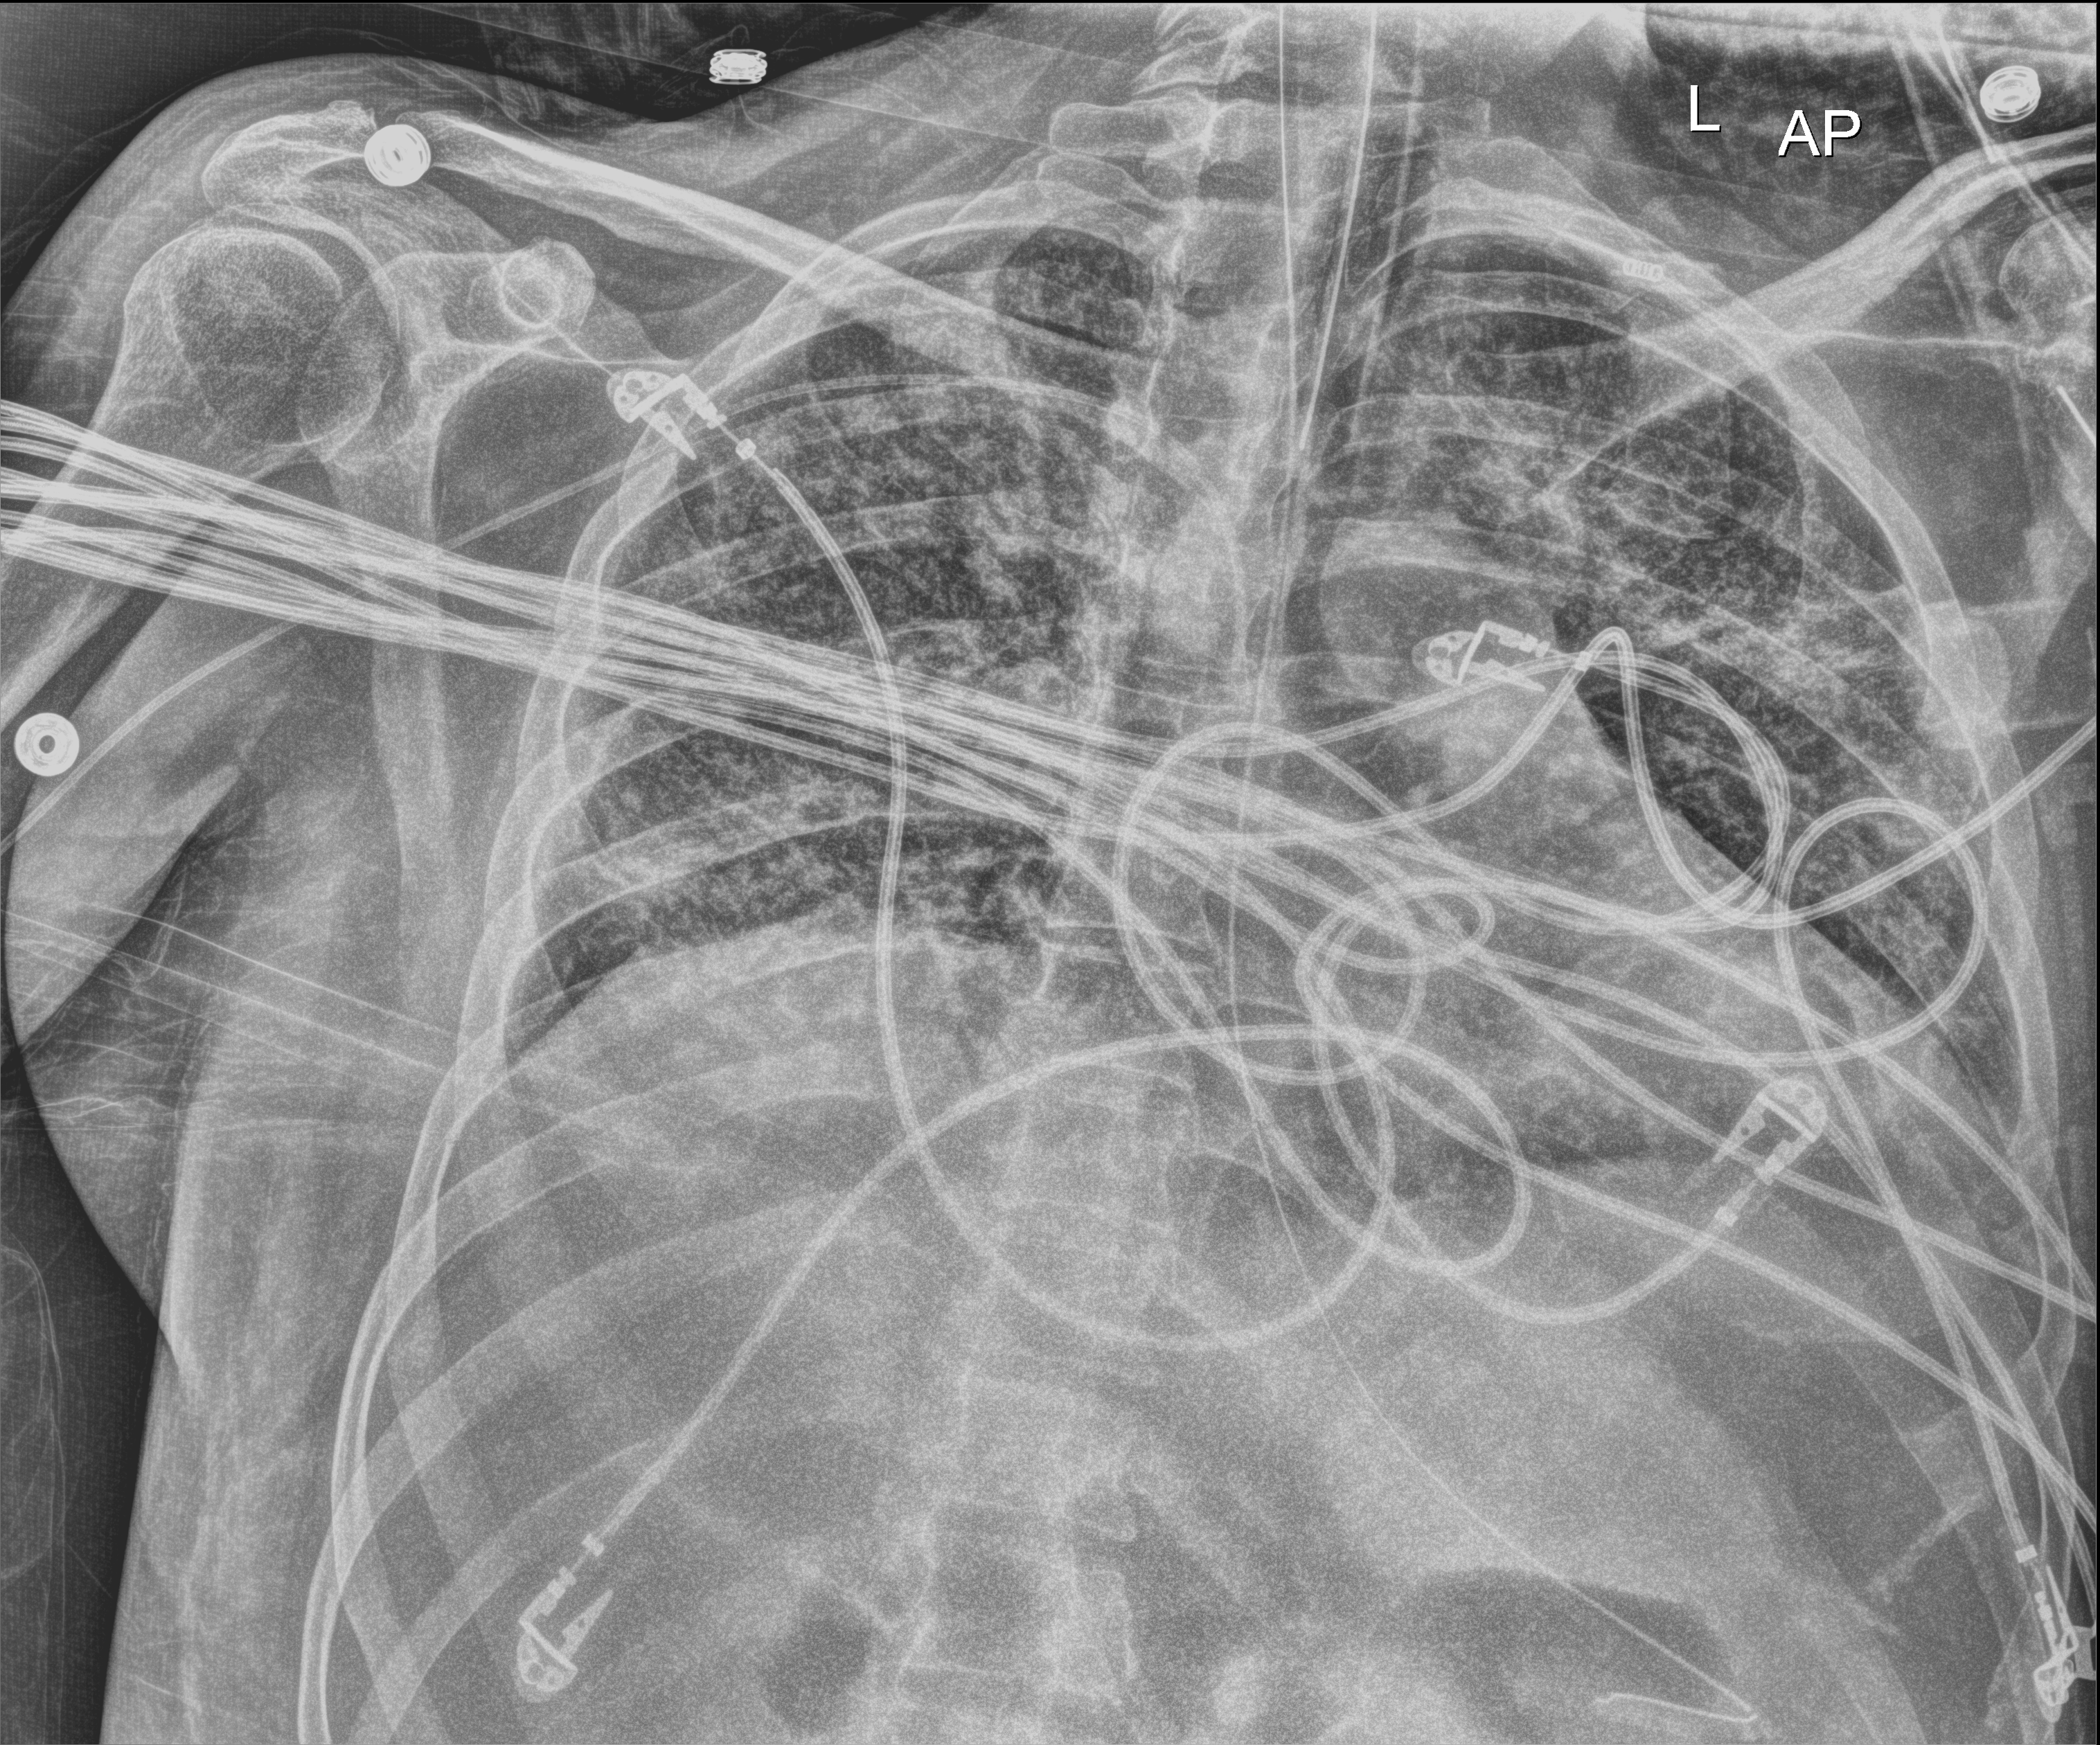
Bedside chest radiograph (digital radiography), anteroposterior (AP) projection. Patient hospitalised with COVID-19; male, aged 18–59 years.
From the hospital-stay record, not from the radiograph (when in the stay this image was taken is not recorded):
- smoking status (admission record): never
- other chronic lung disease (admission record): no